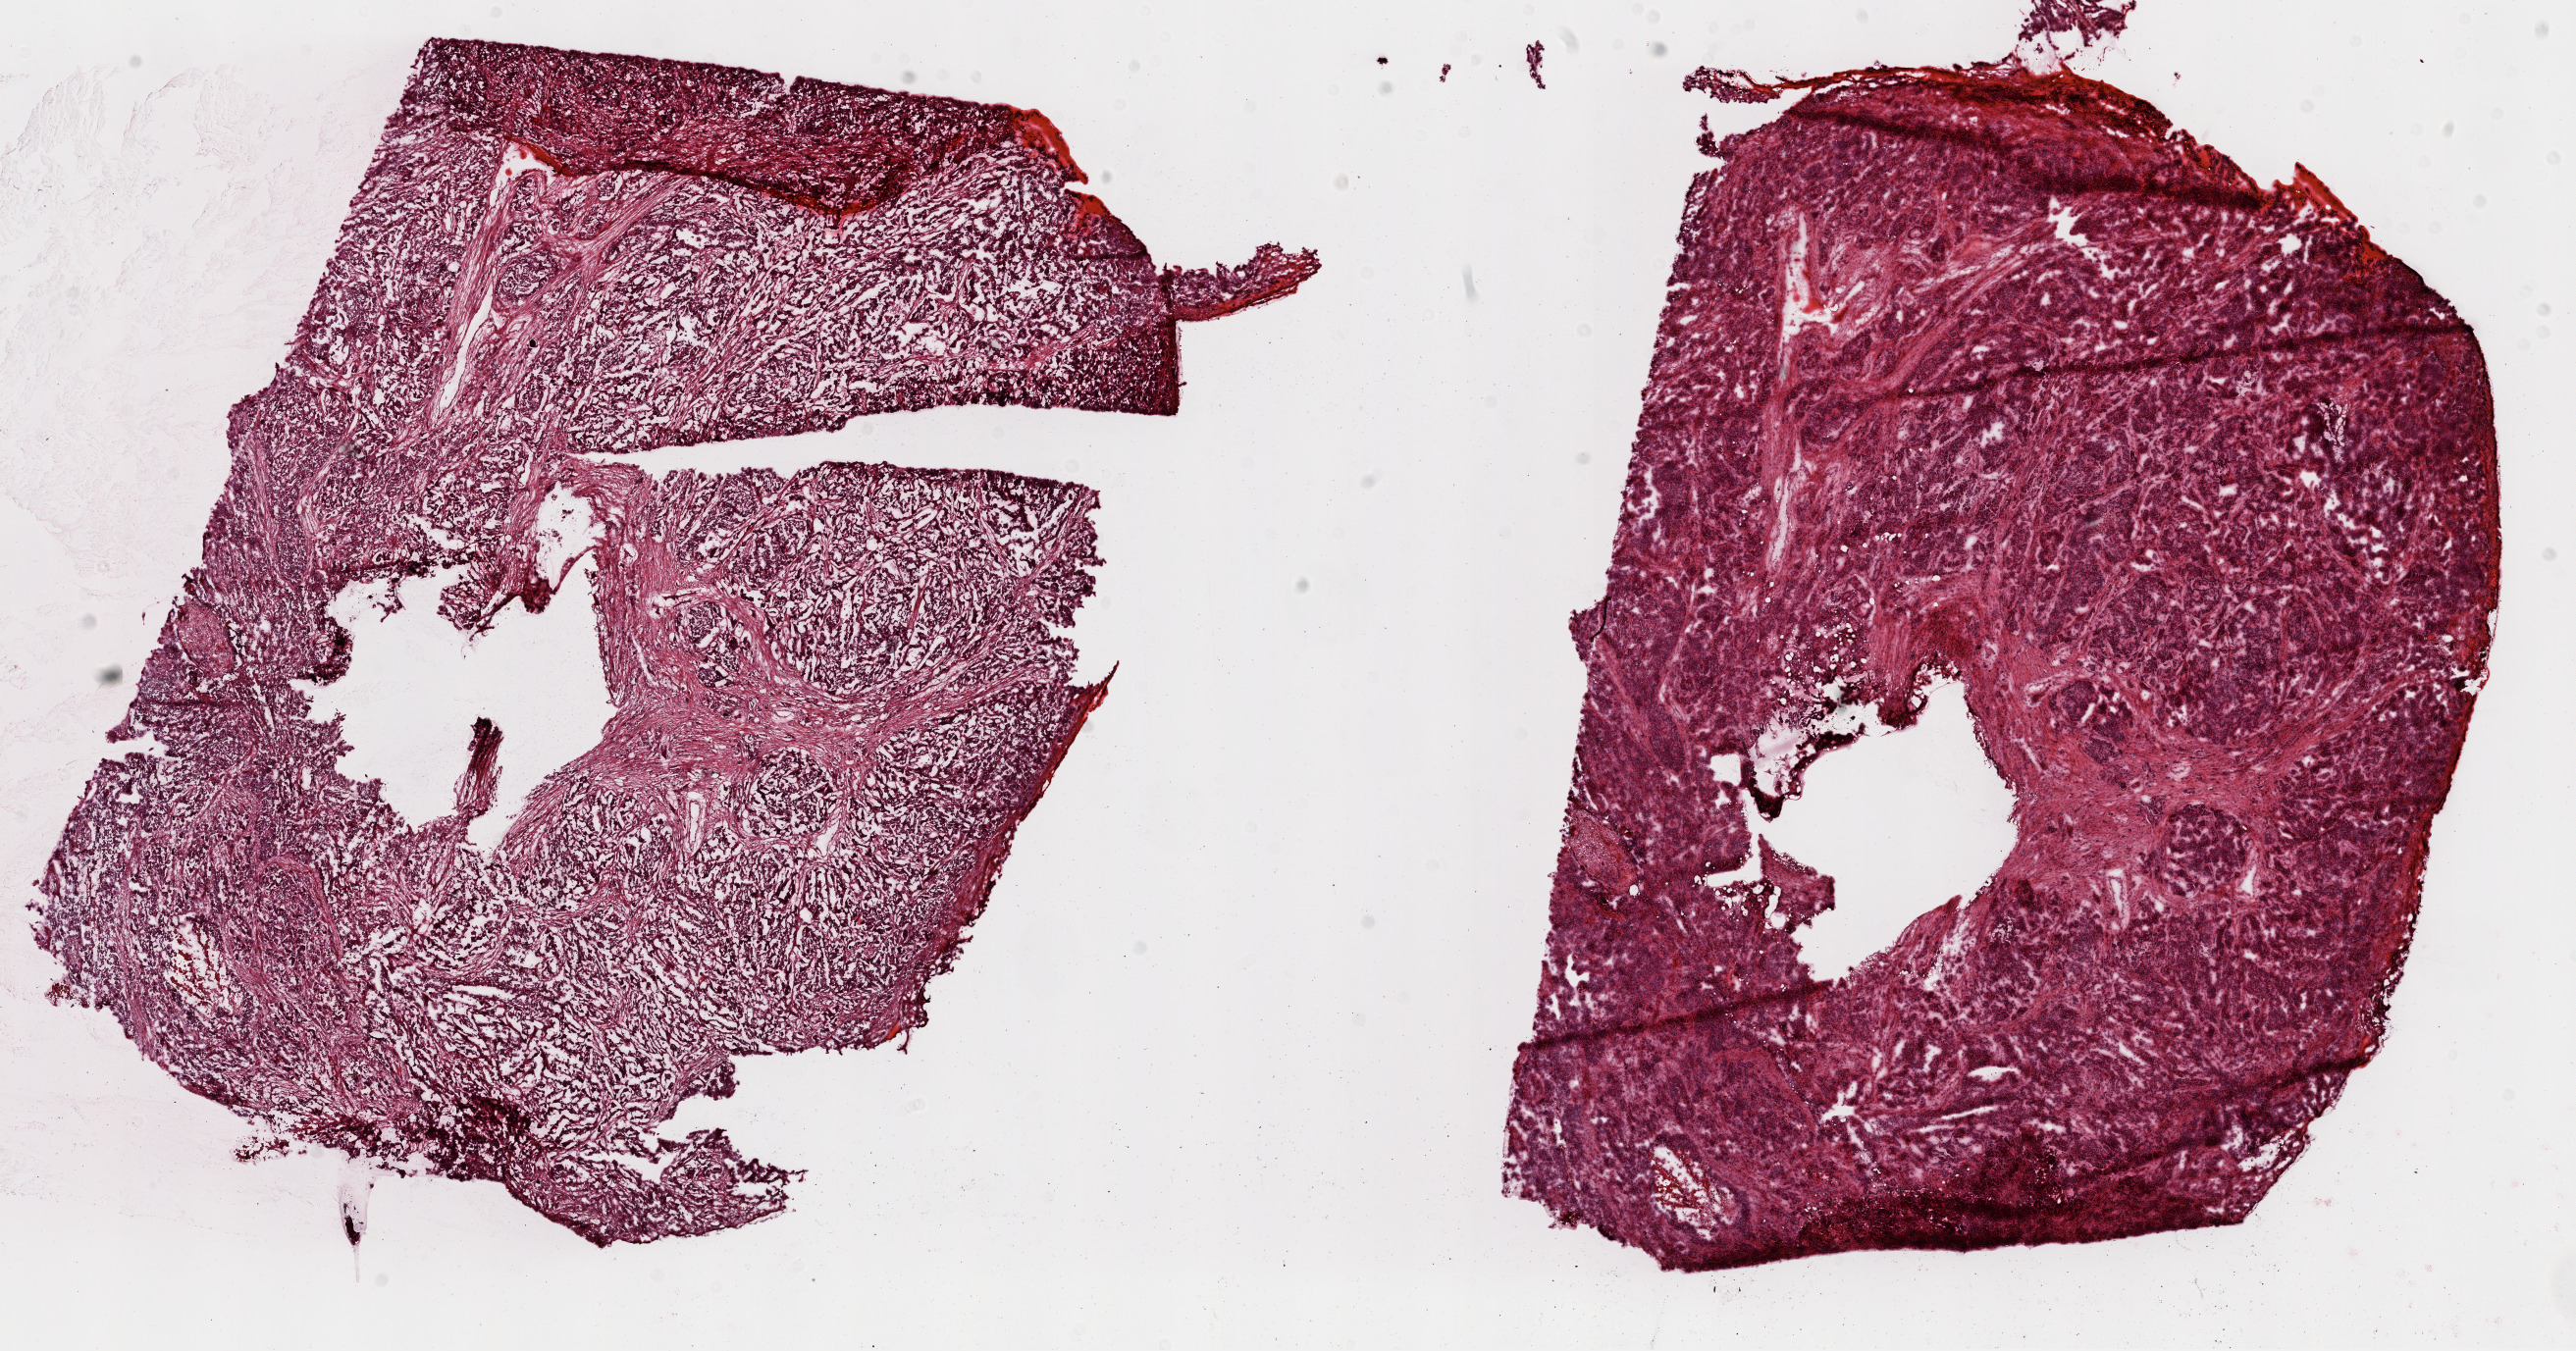
Whole-slide histology image, H&E, shown as a low-resolution overview of the whole scanned area (about 21.1 x 11.0 mm). Frozen section from the top of the tissue portion. Primary tumour sample from the ovary. Patient: female, age at initial diagnosis 77 years. Histologic grade: G3 (poorly differentiated). Pathologist review of this section (percent, as recorded): tumour cells 80%, tumour nuclei 80%, normal cells 0%, stromal cells 15%, necrosis 5%. Infiltration values recorded for this section: lymphocyte infiltration 0%, monocyte infiltration 0%, neutrophil infiltration 5%.
- laterality: bilateral
- FIGO stage: IIIC
- pathologic diagnosis: Serous cystadenocarcinoma, NOS